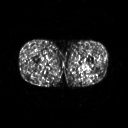
FDG PET of an extremity soft-tissue mass (from a PET/CT study), one axial slice; position 234 of 267 along the scan axis; 128 × 128 image matrix, field of view 500 × 500 mm. Male patient, age 27 years. Case-level facts recorded for this patient, not image findings: histological type: extraskeletal osteosarcoma; grade: high; site of the primary tumour: left adductur.
Annotated regions visible in this slice (expert contour drawn on MRI and transferred to this co-registered scan by the dataset authors):
- gross tumour volume (mass): bounding box [x1, y1, x2, y2] px = [68, 60, 95, 74]